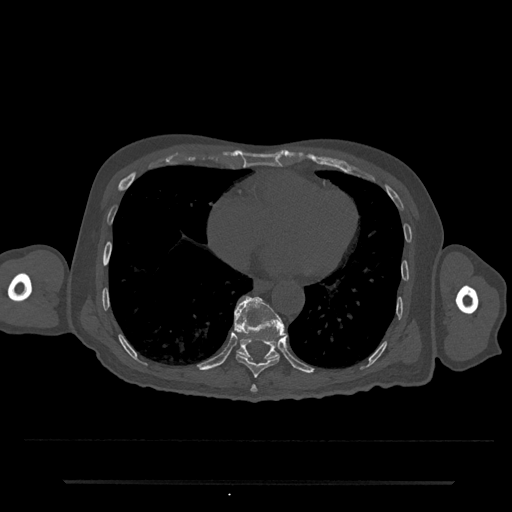
CT including the spine, one axial slice. Slice 346 of 797 in the series (ordered by position). Reconstruction kernel Br40s/3. Bone window (W 1800 / L 400 HU). 0.5 mm slice thickness. 512 × 512 image matrix, field of view 427 × 427 mm. Male patient, age 74 years. From the clinical record (not read from this slice): primary cancer: prostate.
Outlined on this slice (semi-automatic segmentation, software-assisted and operator-edited):
- T10 vertebra: box from (x=234, y=296) to (x=285, y=361) px
- T8 vertebra: (x=250, y=385)–(x=258, y=392)
- T9 vertebra: (x=234, y=310)–(x=285, y=378)